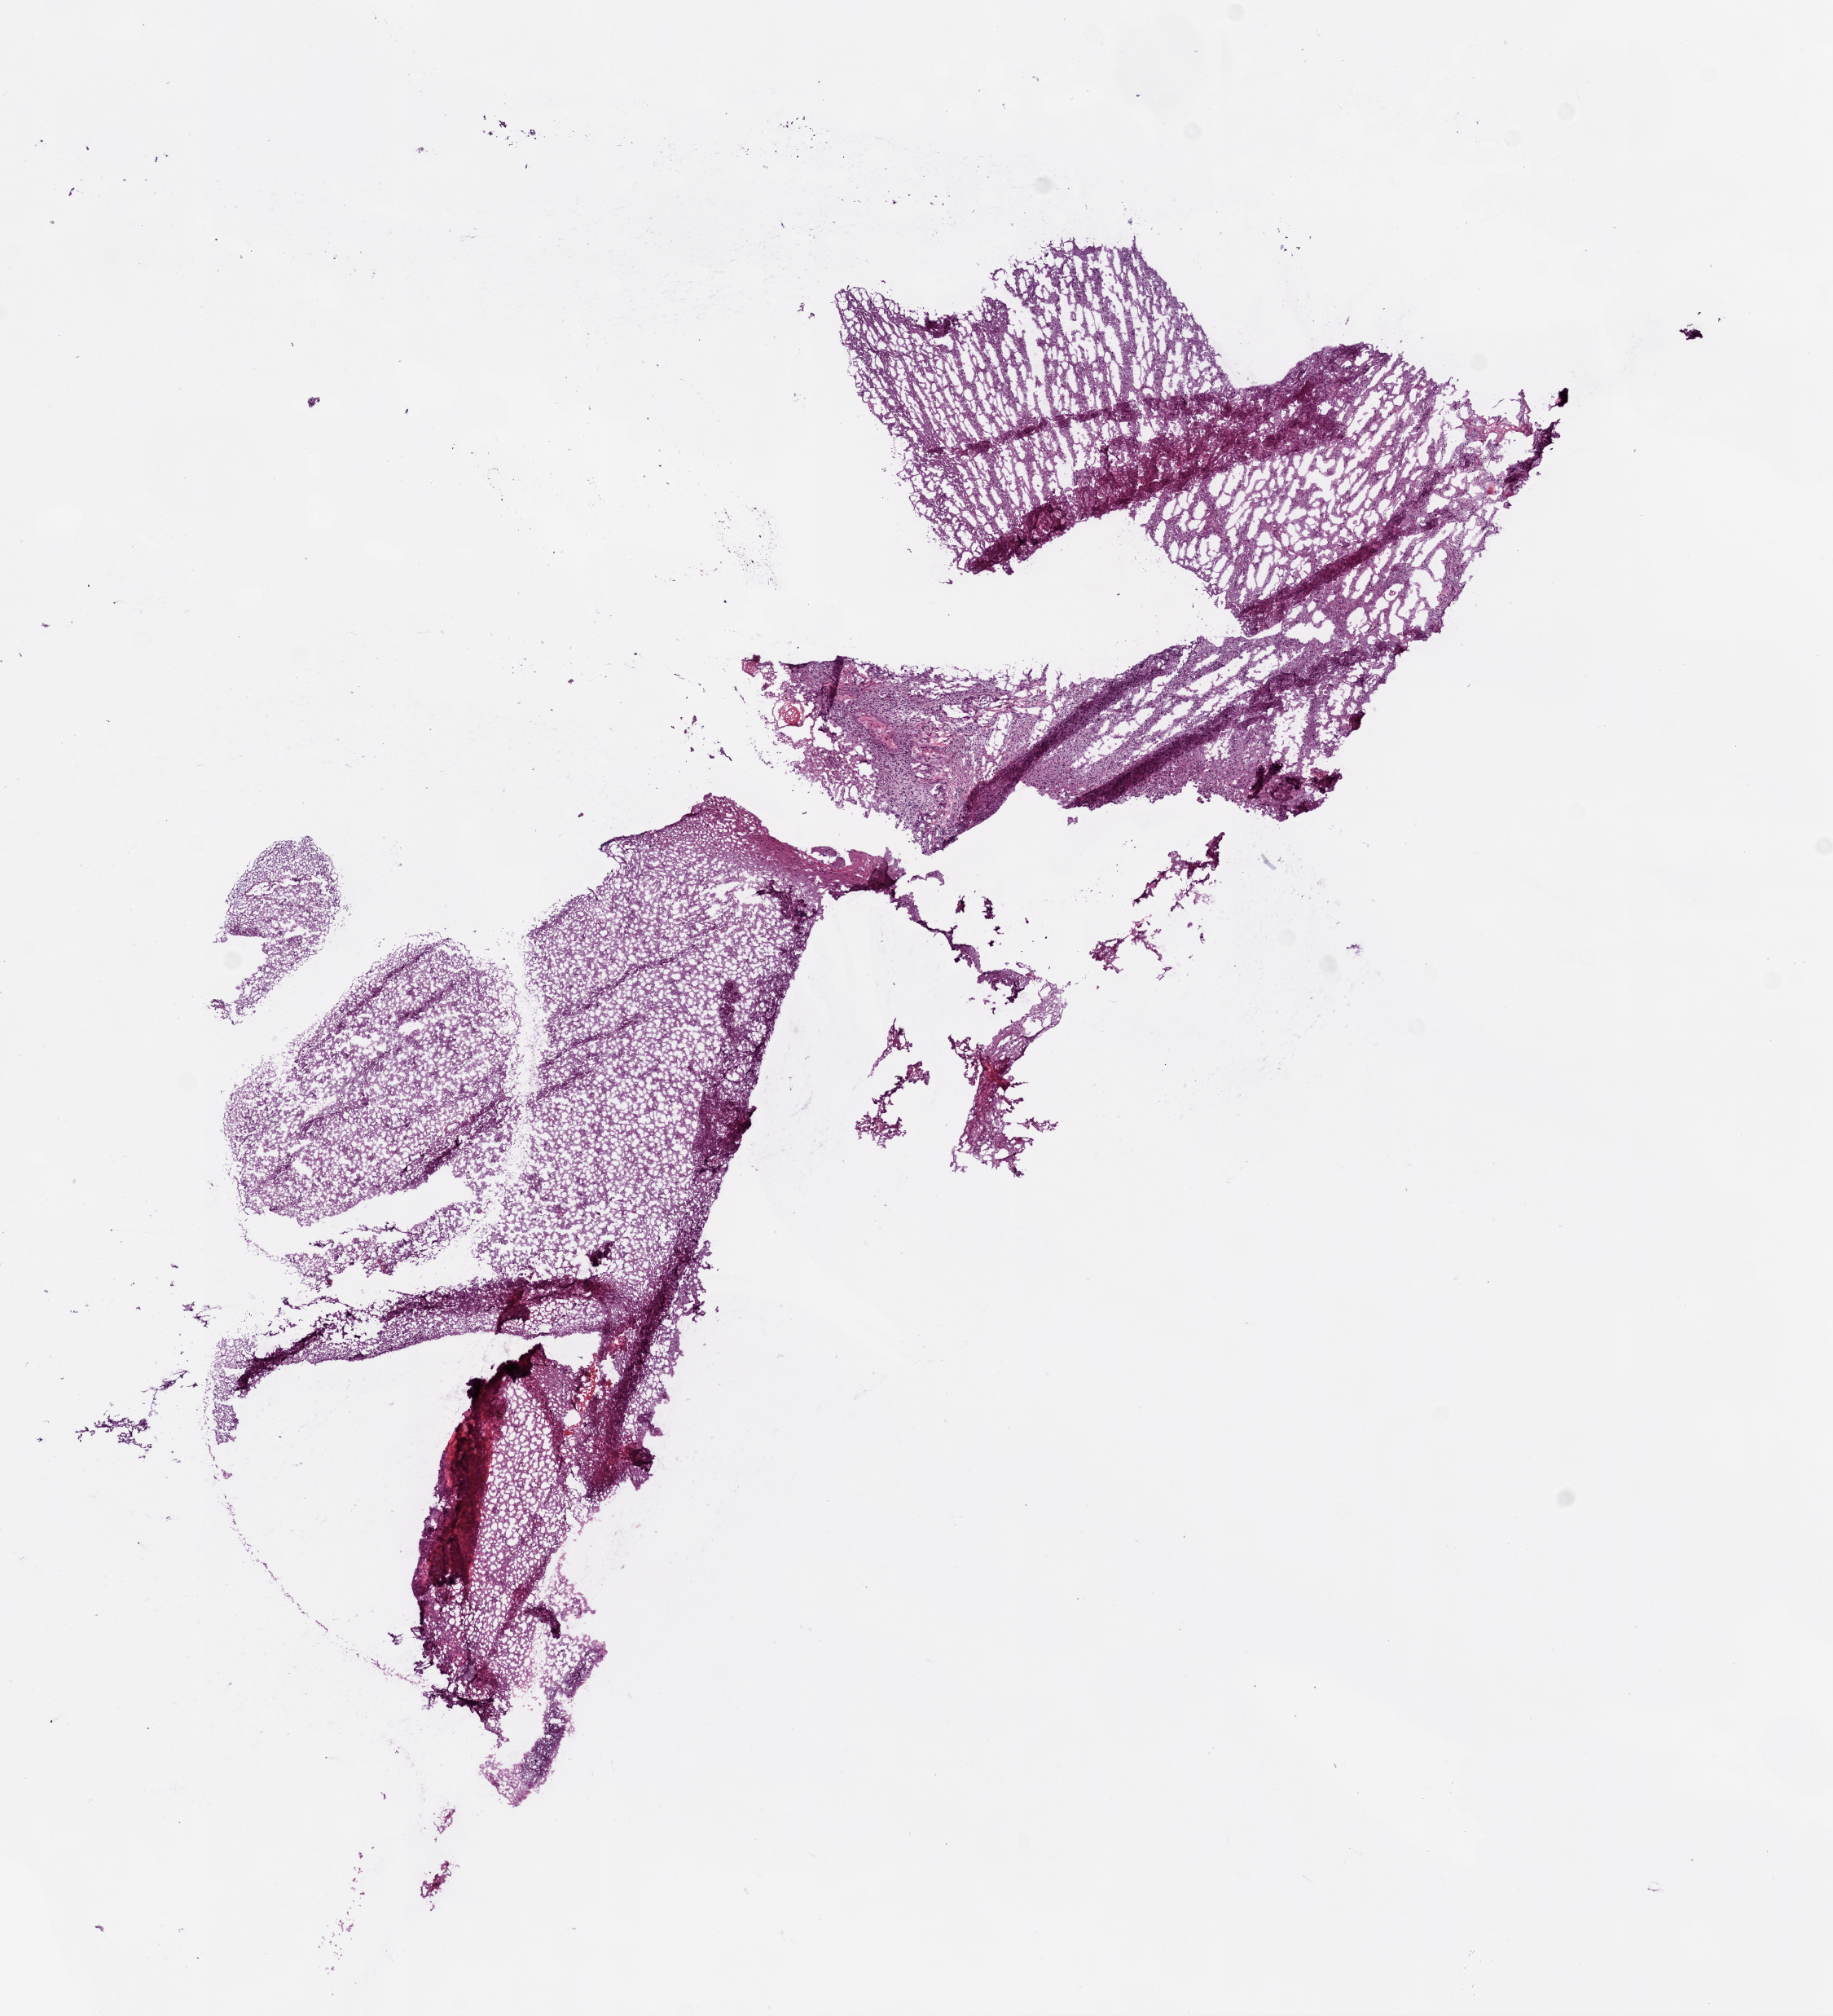
Whole-slide histology image, Hematoxylin and eosin (H&E) stained, a low-resolution overview of the entire scanned area, about 9.0 x 9.9 mm; frozen section from the bottom of the tissue portion; primary tumour sample from the brain. Female, age 33 years at initial diagnosis. Pathologist review of this section (percent, as recorded): tumour cells 80%, tumour nuclei 80%, normal cells 10%, stromal cells 5%, necrosis 5%.
- pathologic diagnosis: Glioblastoma